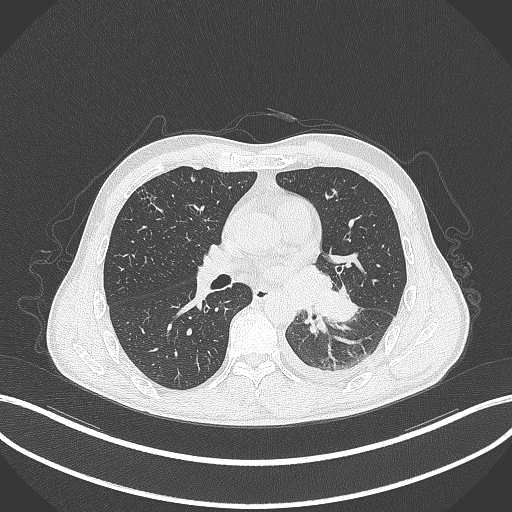
Chest CT, one axial slice; slice 164 of 295 in the series (ordered by position); reconstruction kernel B70f; 120 kVp; lung window (W 1500 / L -600 HU); 1 mm slice thickness; 512 × 512 image matrix. Patient: male, 47 years. From the clinical record (not read from this slice): clinical TNM (as recorded): T3 N1 M1c.
Outlined on this slice (bounding box drawn by a radiologist):
- lung tumour (recorded histology: small cell carcinoma): box from (x=316, y=282) to (x=359, y=325) px